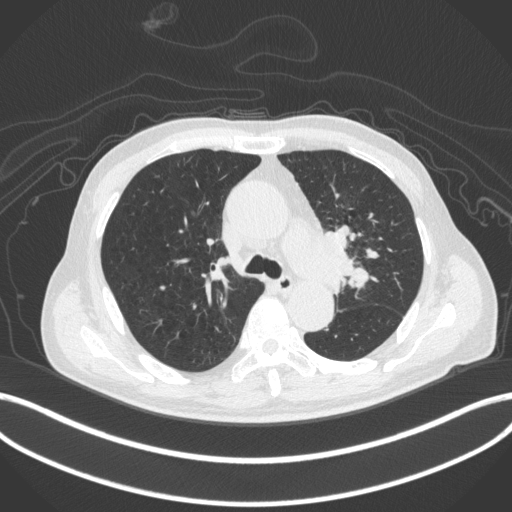
Chest CT, one axial slice; slice 290 of 420 in the series (ordered by position); reconstruction kernel B31f; 120 kVp; lung window (W 1500 / L -600 HU); 1 mm slice thickness; 512 × 512 image matrix, field of view 400 × 400 mm. Male patient, age 77 years. From the clinical record (not read from this slice): clinical TNM (as recorded): T3 N1 M0.
Annotated regions visible in this slice (rectangle marked by the reading radiologist):
- lung tumour (recorded histology: adenocarcinoma): box from (x=313, y=224) to (x=363, y=293) px